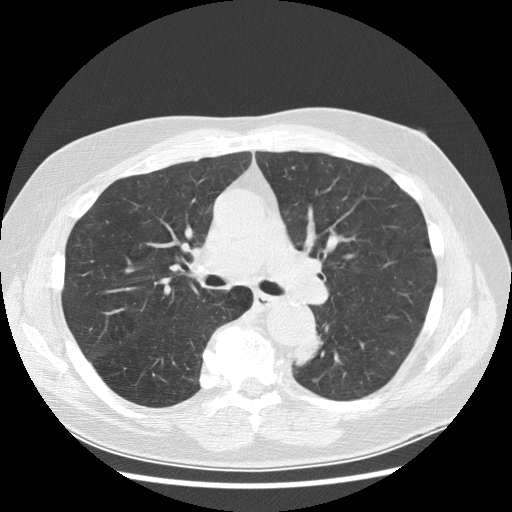
Low-dose screening chest CT, one axial slice. Reconstruction kernel STANDARD. 120 kVp. Lung window (W 1500 / L -600 HU). 2.5 mm slice thickness. 512 × 512 image matrix.
Structures marked on this image (manually delineated by an expert):
- lesion 1 (tumor, lower lobe of left lung): box from (x=295, y=333) to (x=323, y=366) px